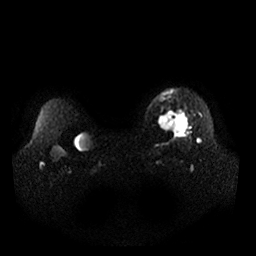
Breast MRI, one axial slice; position 28 of 32 along the scan axis; diffusion-weighted series; image 2 of 4 stored at this slice position (different b-values; order by instance number); 1.5 T; 4 mm slice thickness; 256 × 256 image matrix. Female patient.
Annotated regions visible in this slice (manually delineated by an expert):
- tumour on diffusion-weighted imaging: box from (x=158, y=110) to (x=189, y=133) px